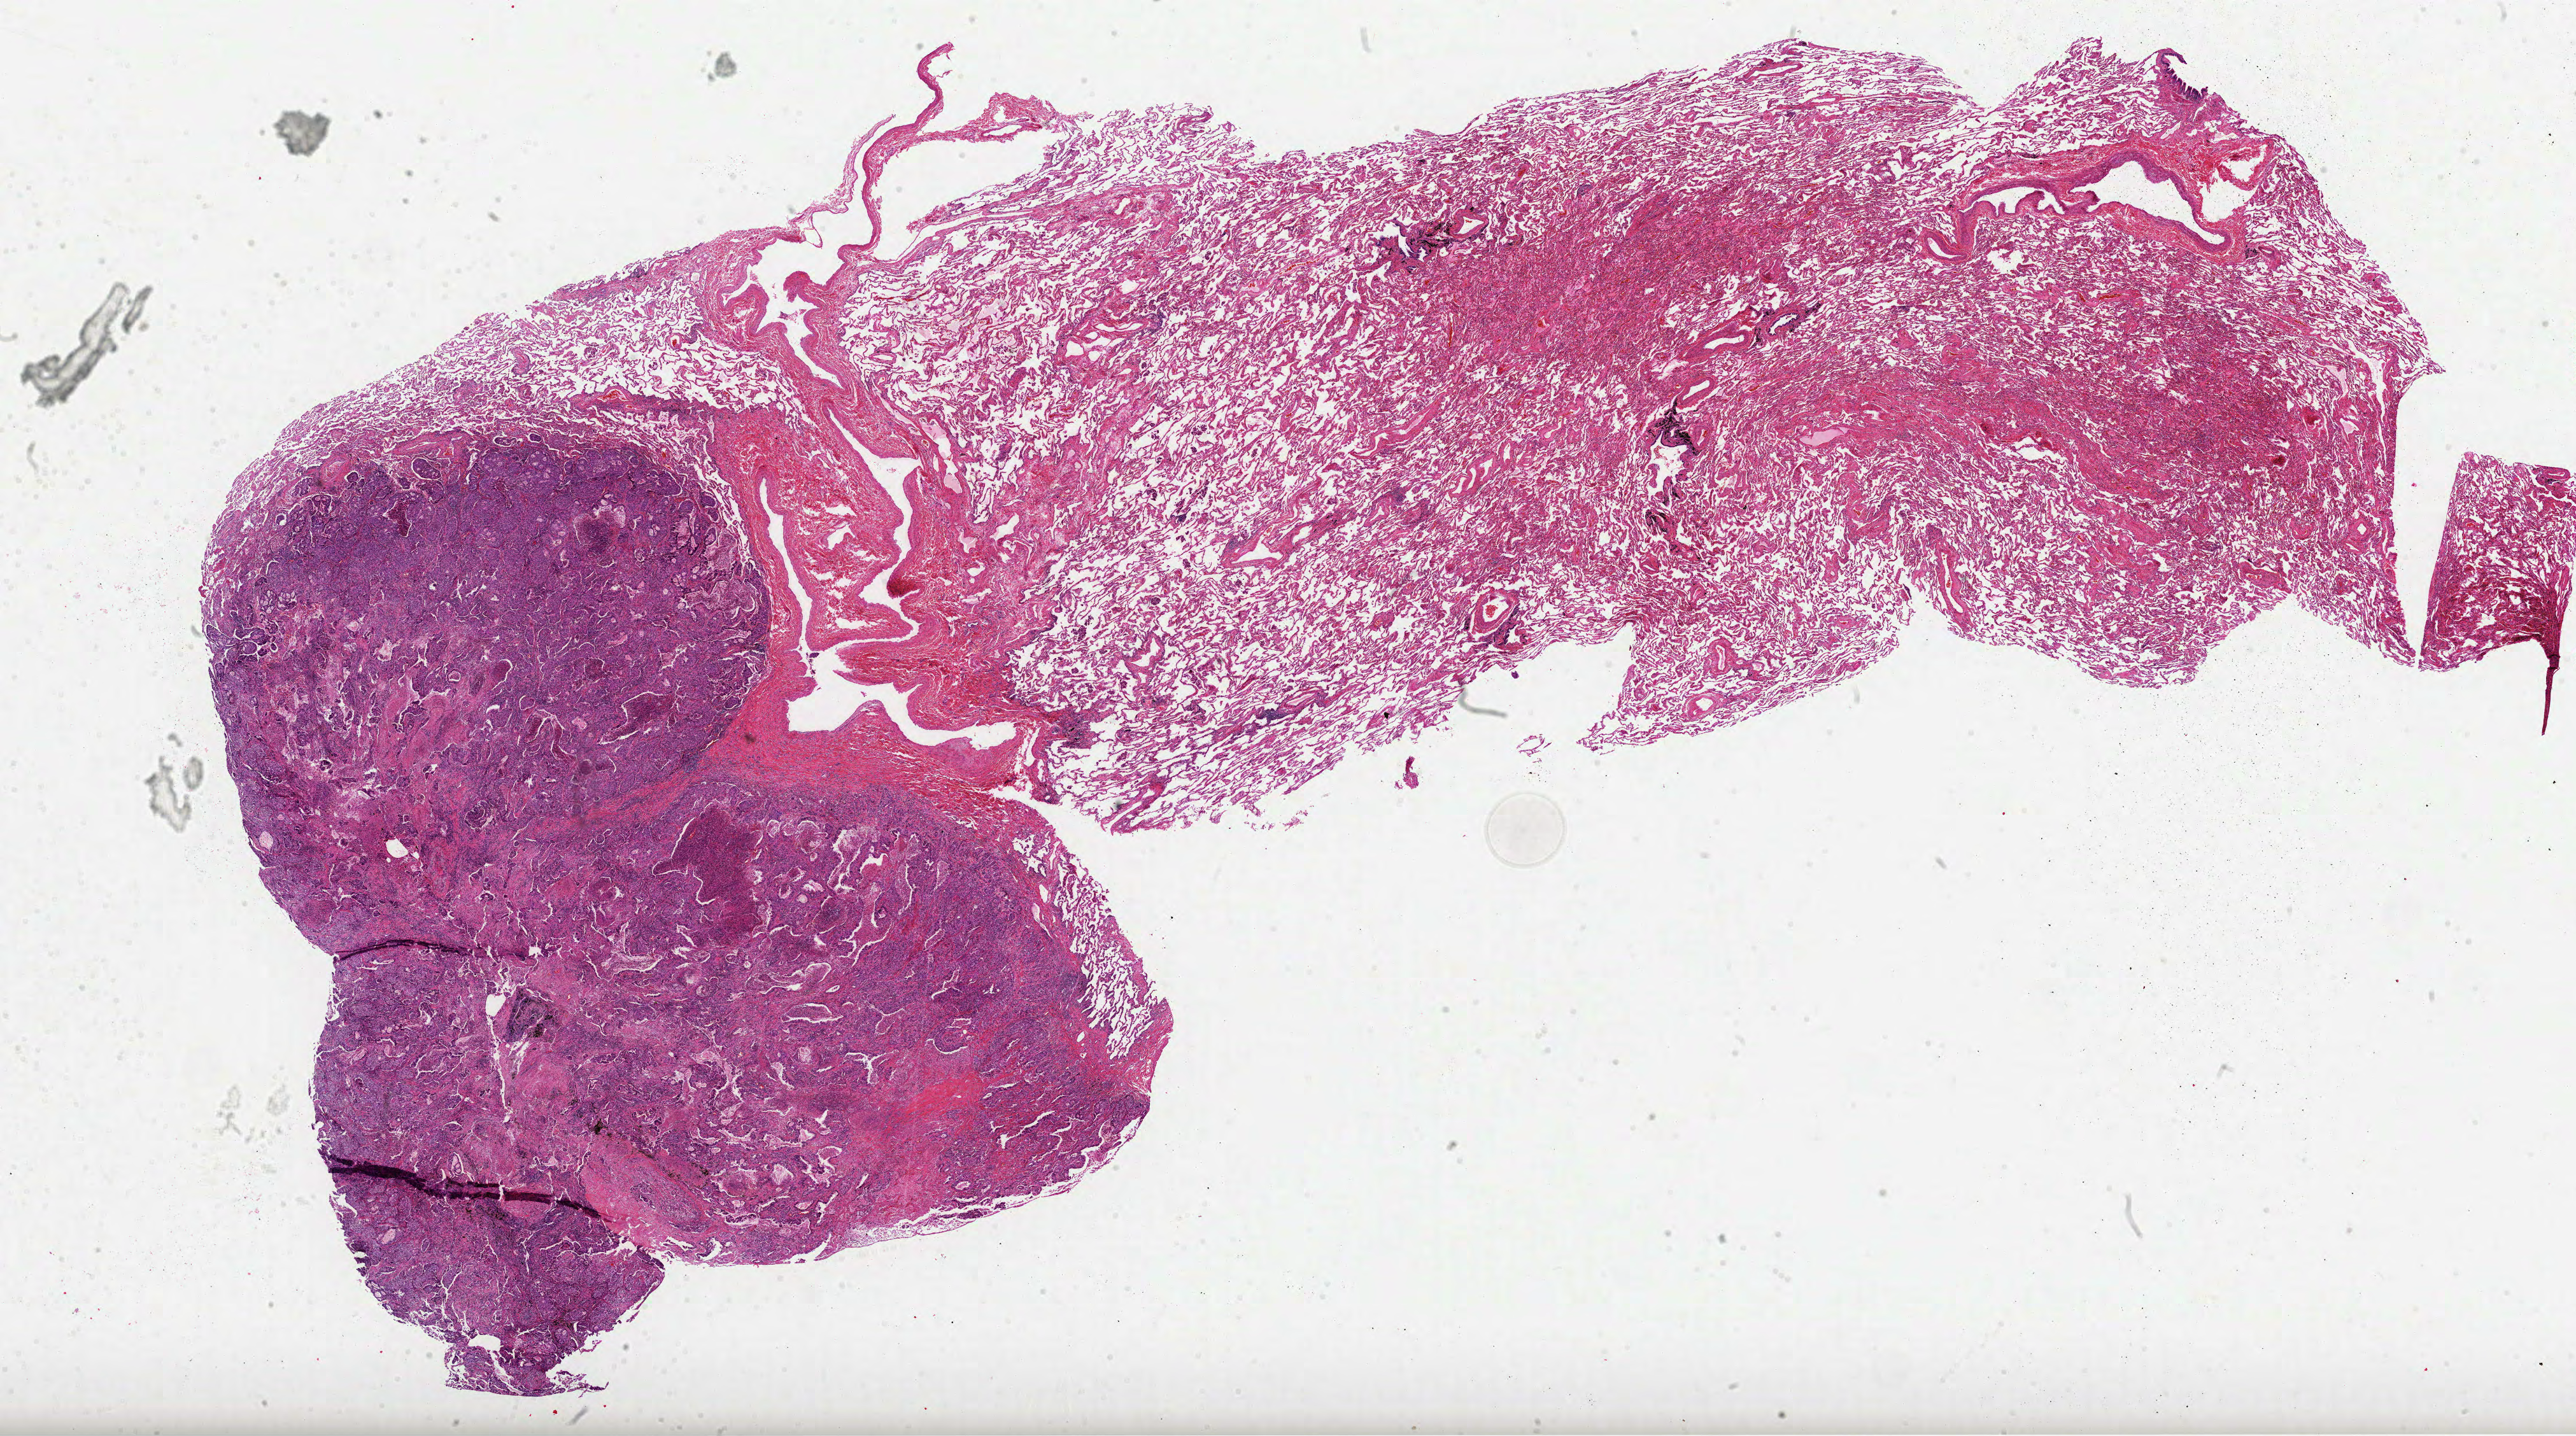
H&E-stained whole-slide image, shown as a low-resolution overview of the whole scanned area (about 32.6 x 18.2 mm, slide scanned at 40x). Formalin-fixed paraffin-embedded (FFPE) diagnostic section. Sample: primary tumour, lung. Male, age 77 years at initial diagnosis.
Pathologic diagnosis: Adenocarcinoma, NOS (upper lobe, lung). AJCC pathologic stage: IIIA. TNM: T3 N2 M0.